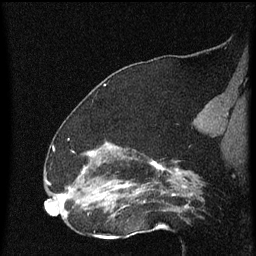
Breast MRI (dynamic contrast-enhanced), one sagittal slice; slice 36 of 60 in the series (ordered by position); dynamic contrast-enhanced series, image 2 of 4 at this slice position (ordered by acquisition); 1.5 T; TE 4.2 ms, TR 8 ms; 2 mm slice thickness; 256 × 256 image matrix, field of view 180 × 180 mm. Patient: female, 52 years.
Outlined on this slice (semi-automatic segmentation, software-assisted and operator-edited):
- analysis volume of interest (the breast-tissue region the enhancement analysis was run in; not a lesion): box from (x=73, y=148) to (x=172, y=219) px
- tumour enhancement mask (voxels above the 70 % enhancement threshold inside the analysis volume of interest): (x=83, y=152)–(x=165, y=209)